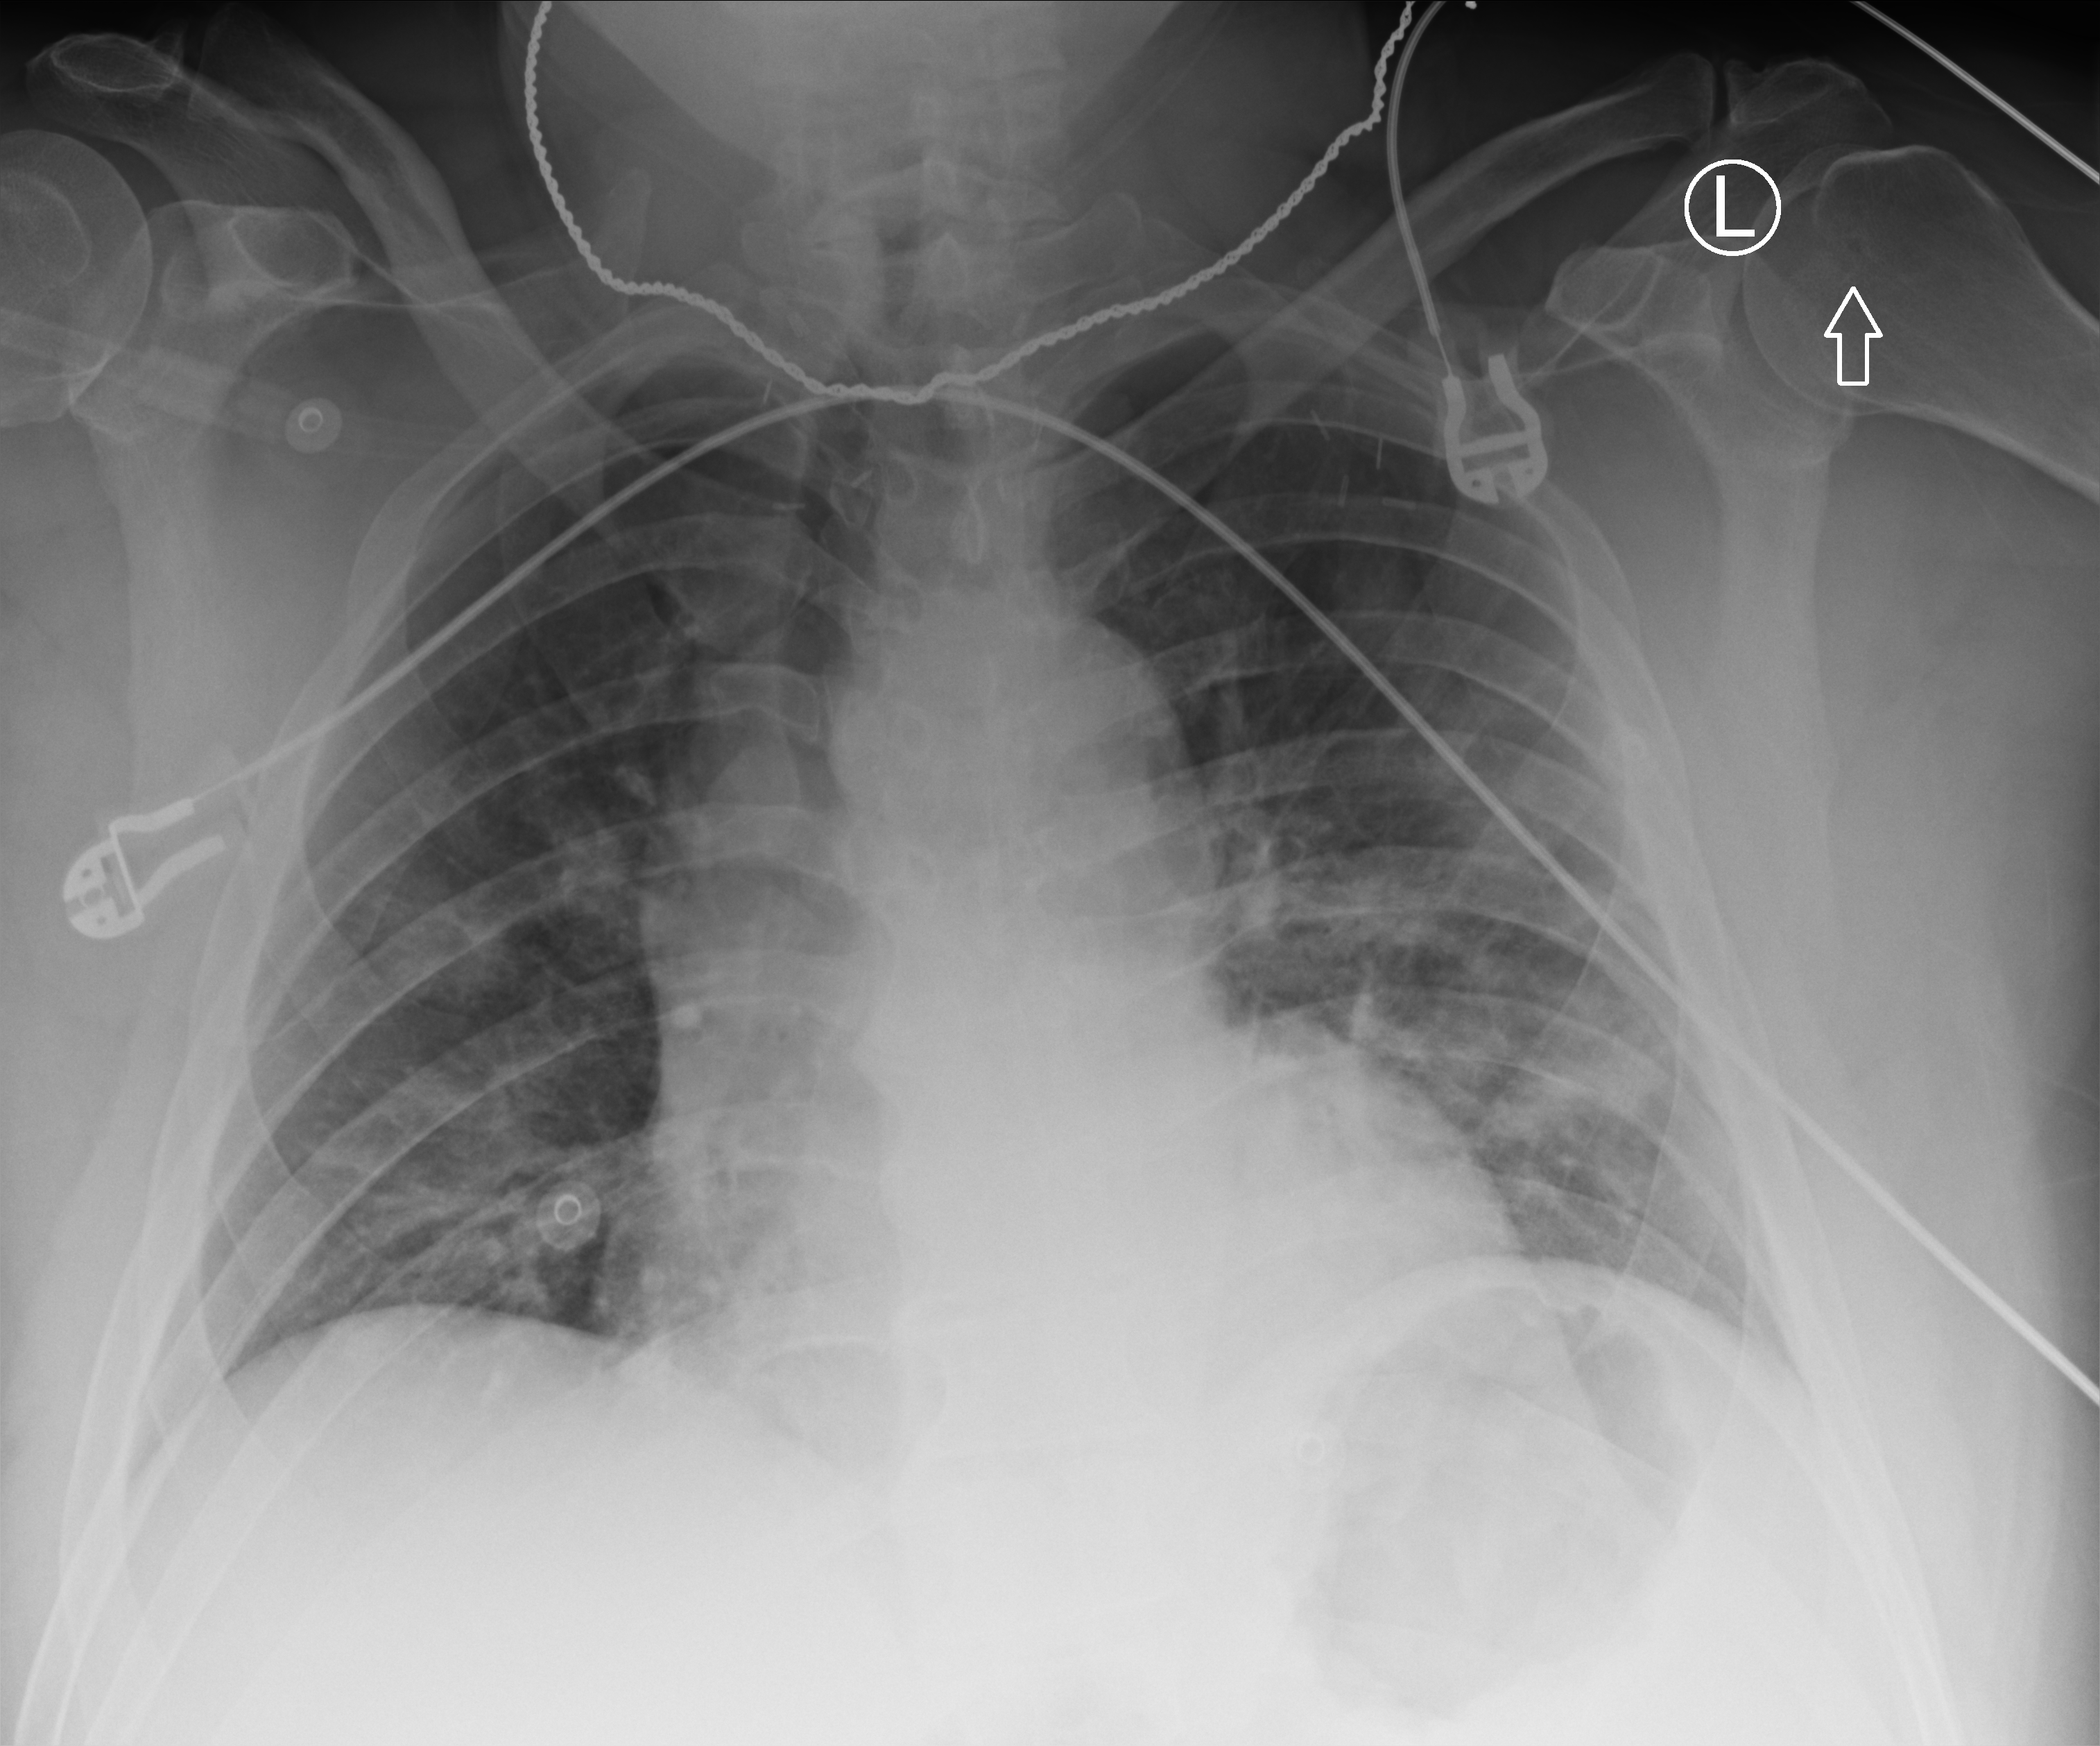
Bedside chest radiograph (computed radiography), anteroposterior (AP) projection. Patient hospitalised with COVID-19, aged 18–59 years.
Hospital-stay facts (about this admission, not read from this image; timing relative to this image not recorded): smoking status (admission record): never; mechanically ventilated during this hospital stay: yes.